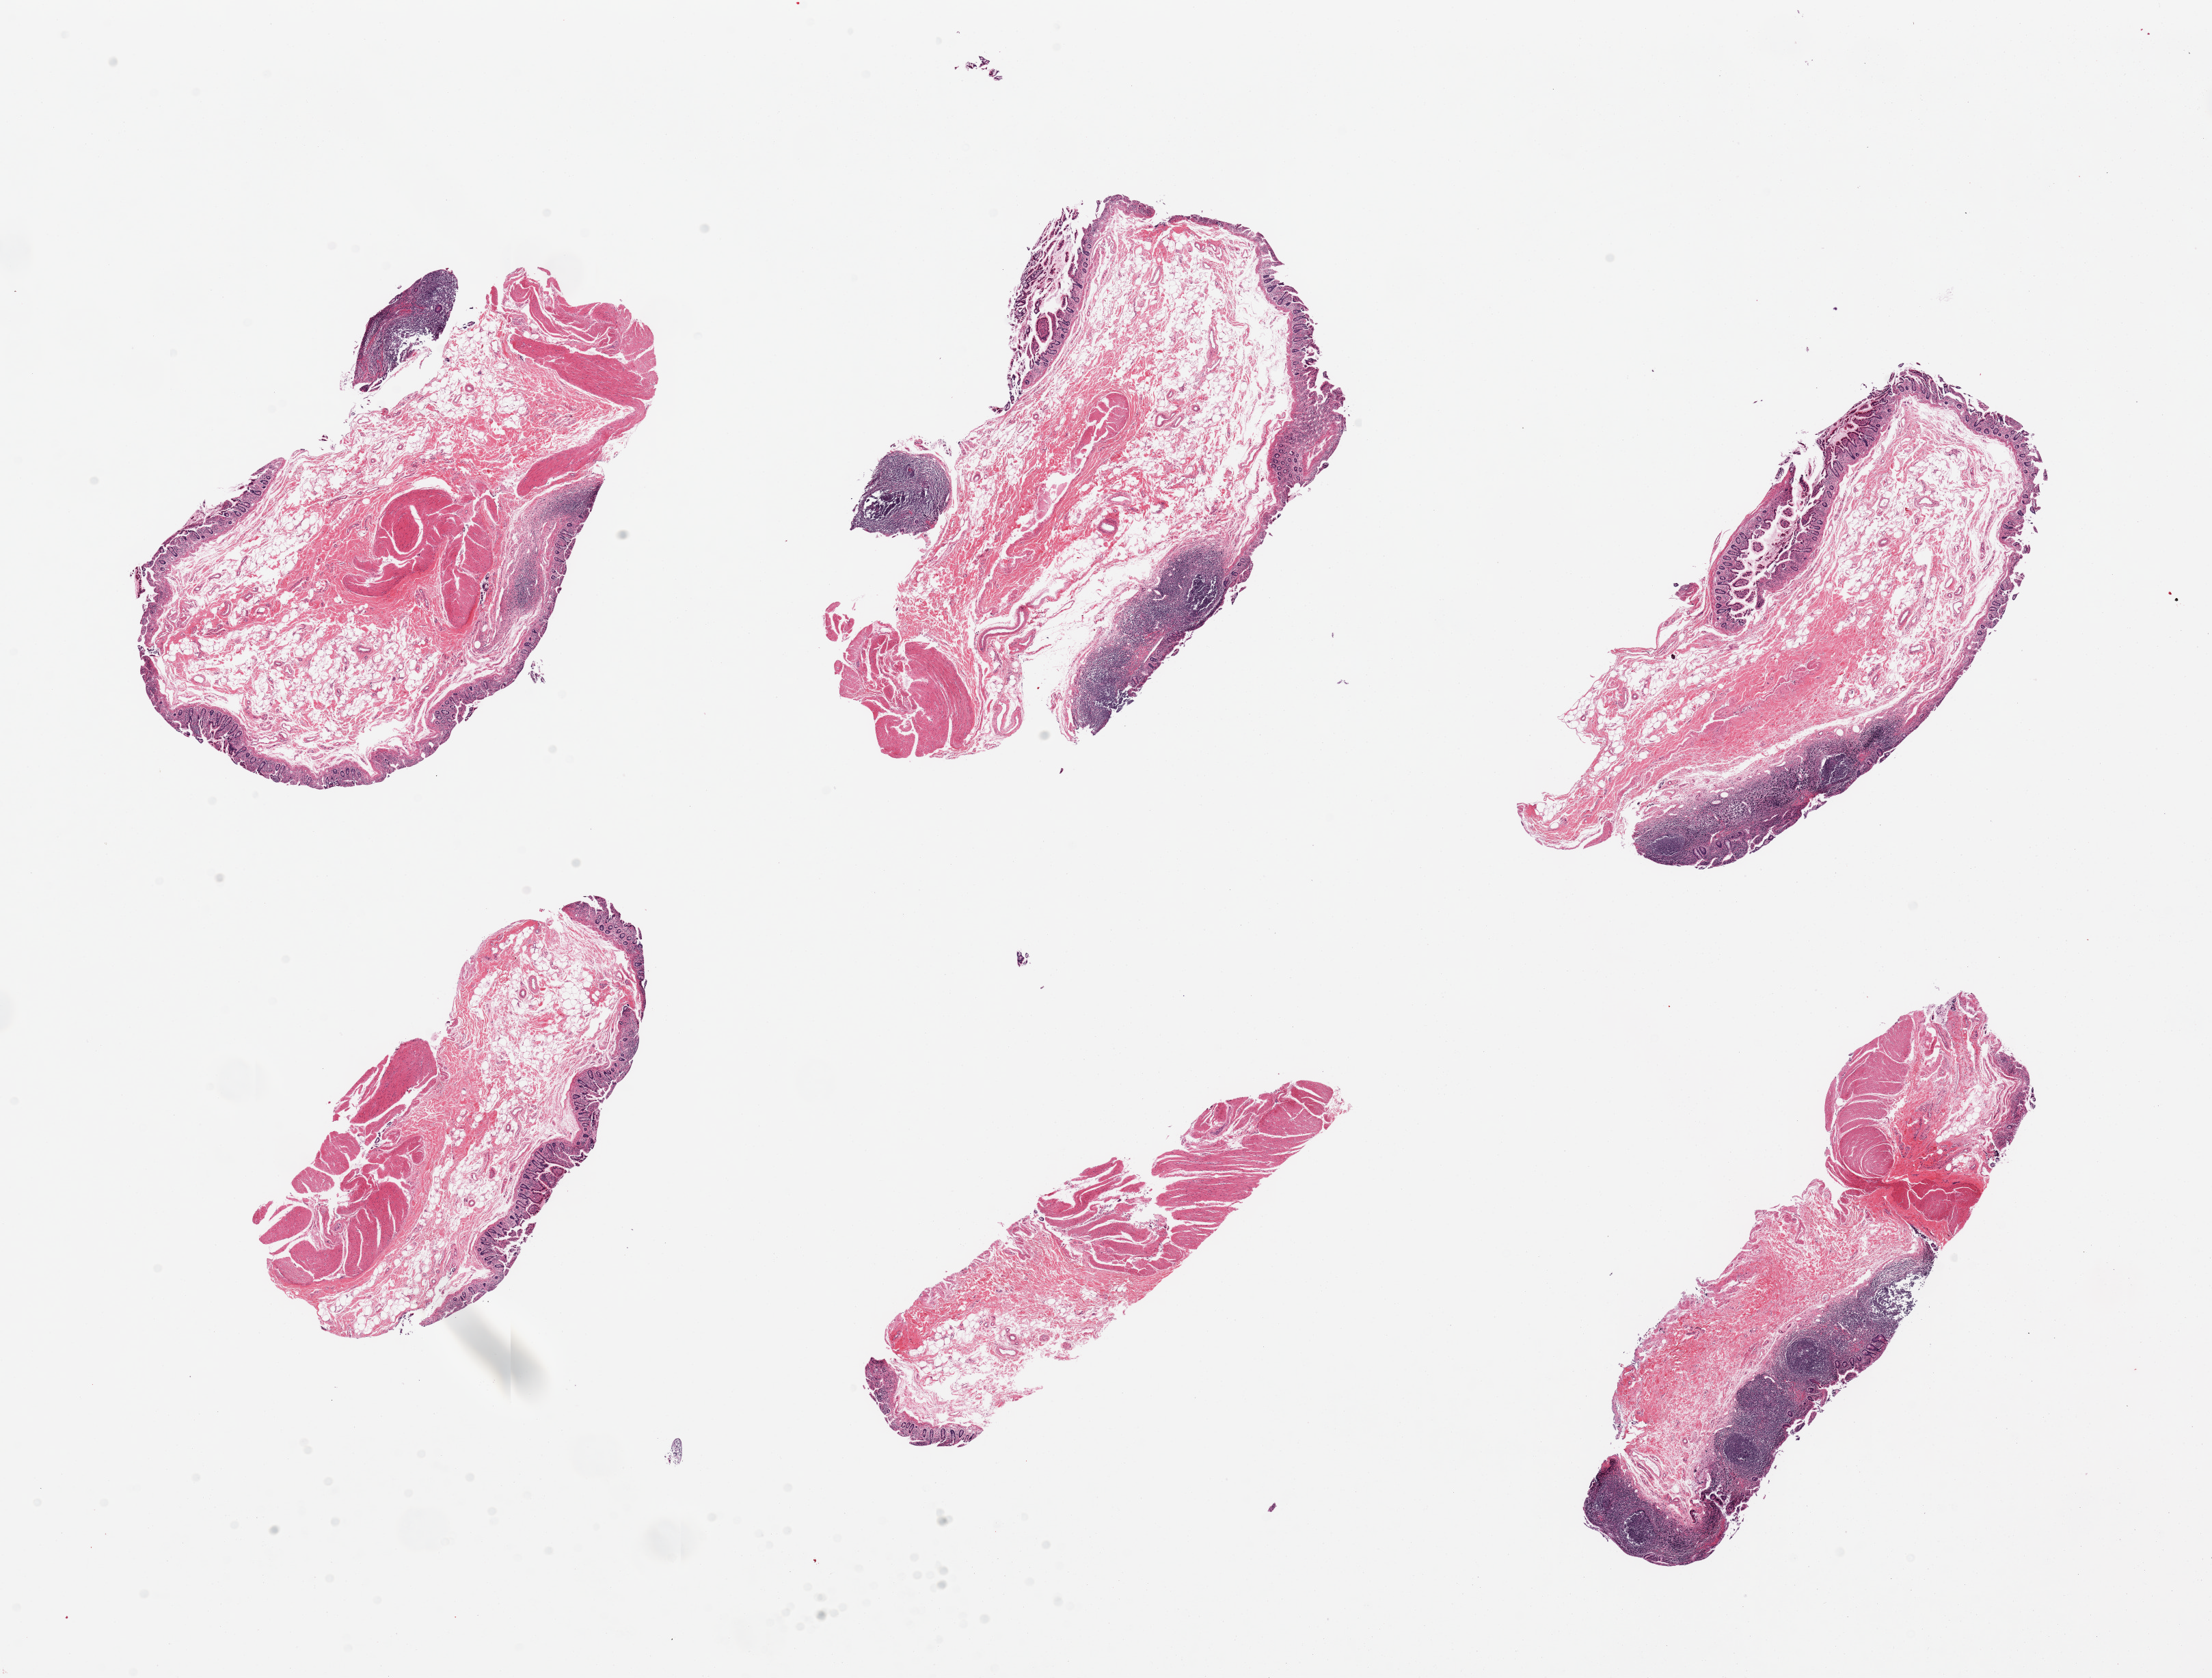
Digitized hematoxylin and eosin (H&E)-stained section, brightfield — whole scanned area (about 25.6 x 19.4 mm) shown as a low-resolution overview. PAXgene-fixed, paraffin-embedded tissue. Section of ileum (target tissue). Donor tissue sample. Donor: male.
Pathologist's review note for this sample: 6 pieces, lymphoid aggregates well- represented, ~10% total tissue.